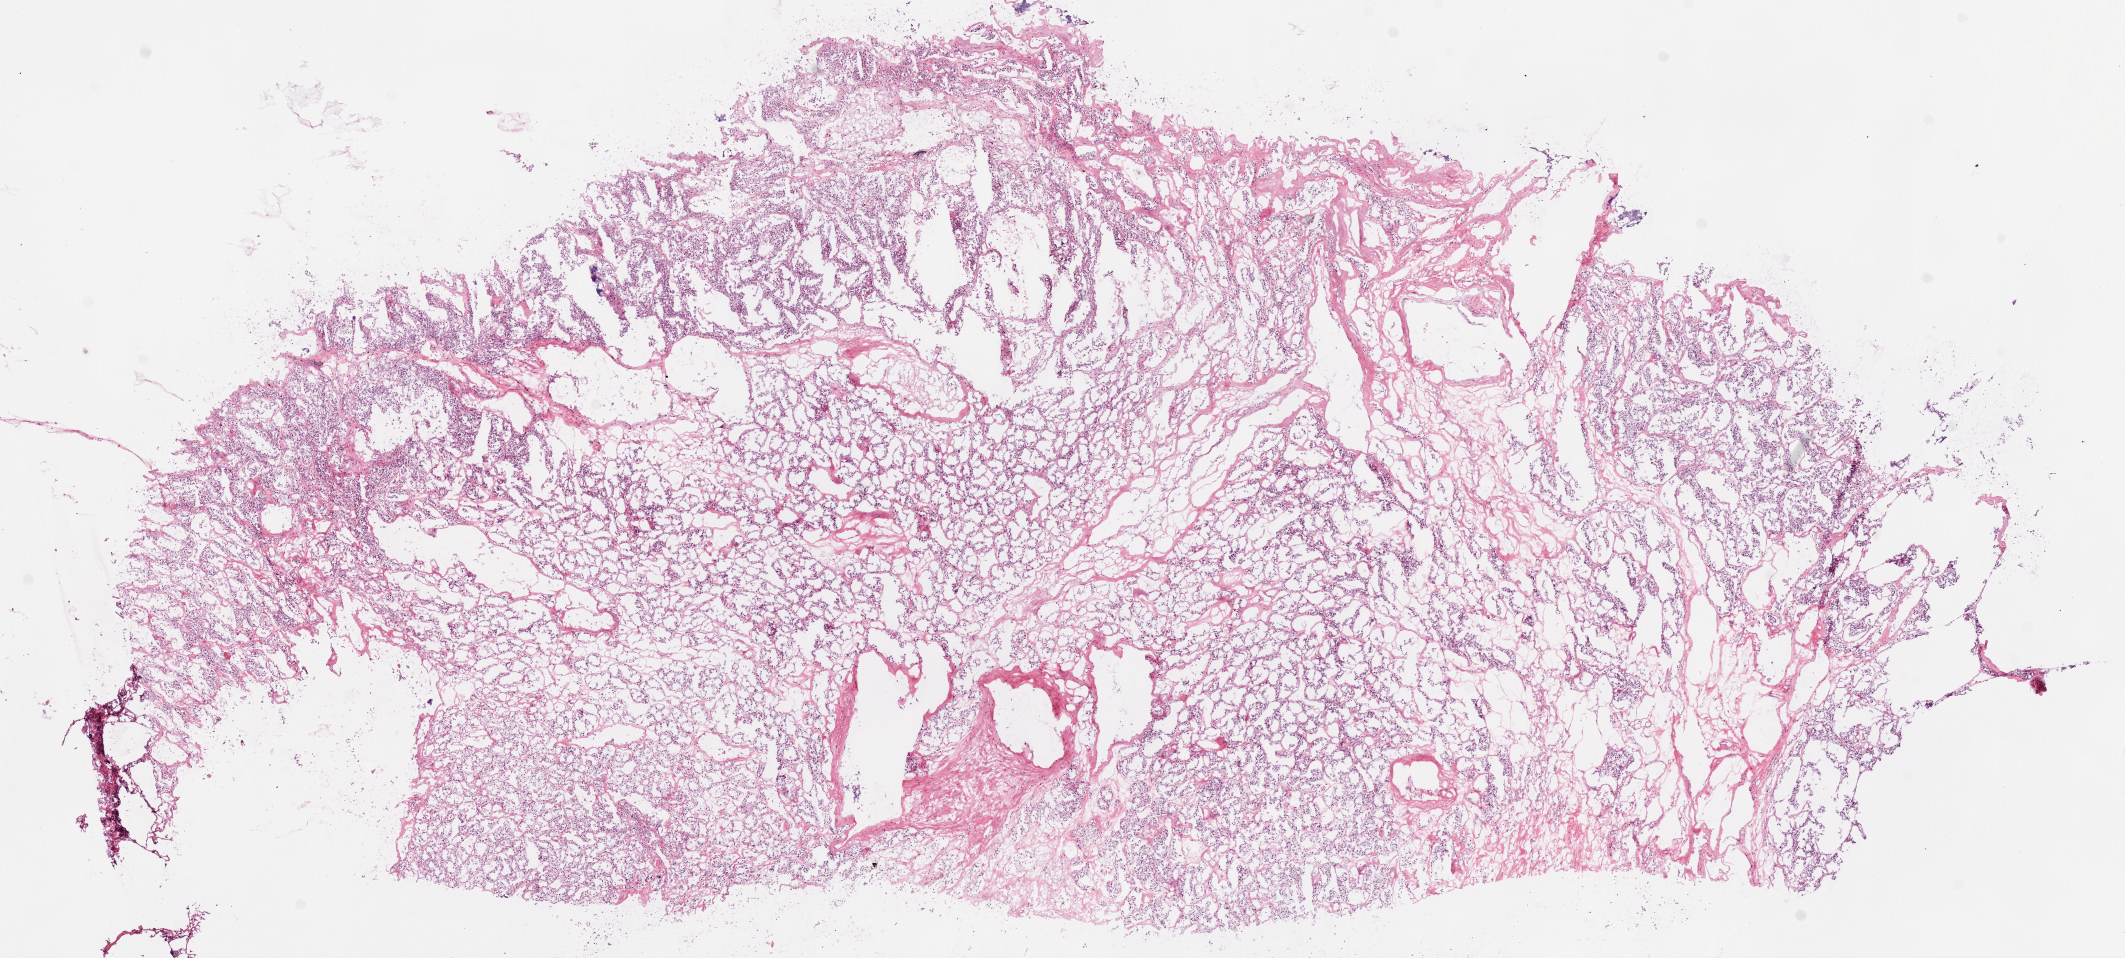
Hematoxylin and eosin (H&E) stained whole-slide image — whole scanned area (about 17.1 x 7.7 mm, slide scanned at 20x) shown as a low-resolution overview. Frozen section from the top of the tissue portion. Sample: primary tumour, kidney. Female patient; age at initial diagnosis 74 years. Histologic grade: G3 (poorly differentiated). Slide review estimates, as recorded: tumour cells 85%, tumour nuclei 80%, normal cells 0%, stromal cells 15%, necrosis 0%.
Histologic diagnosis: Clear cell adenocarcinoma, NOS. AJCC pathologic stage: I.